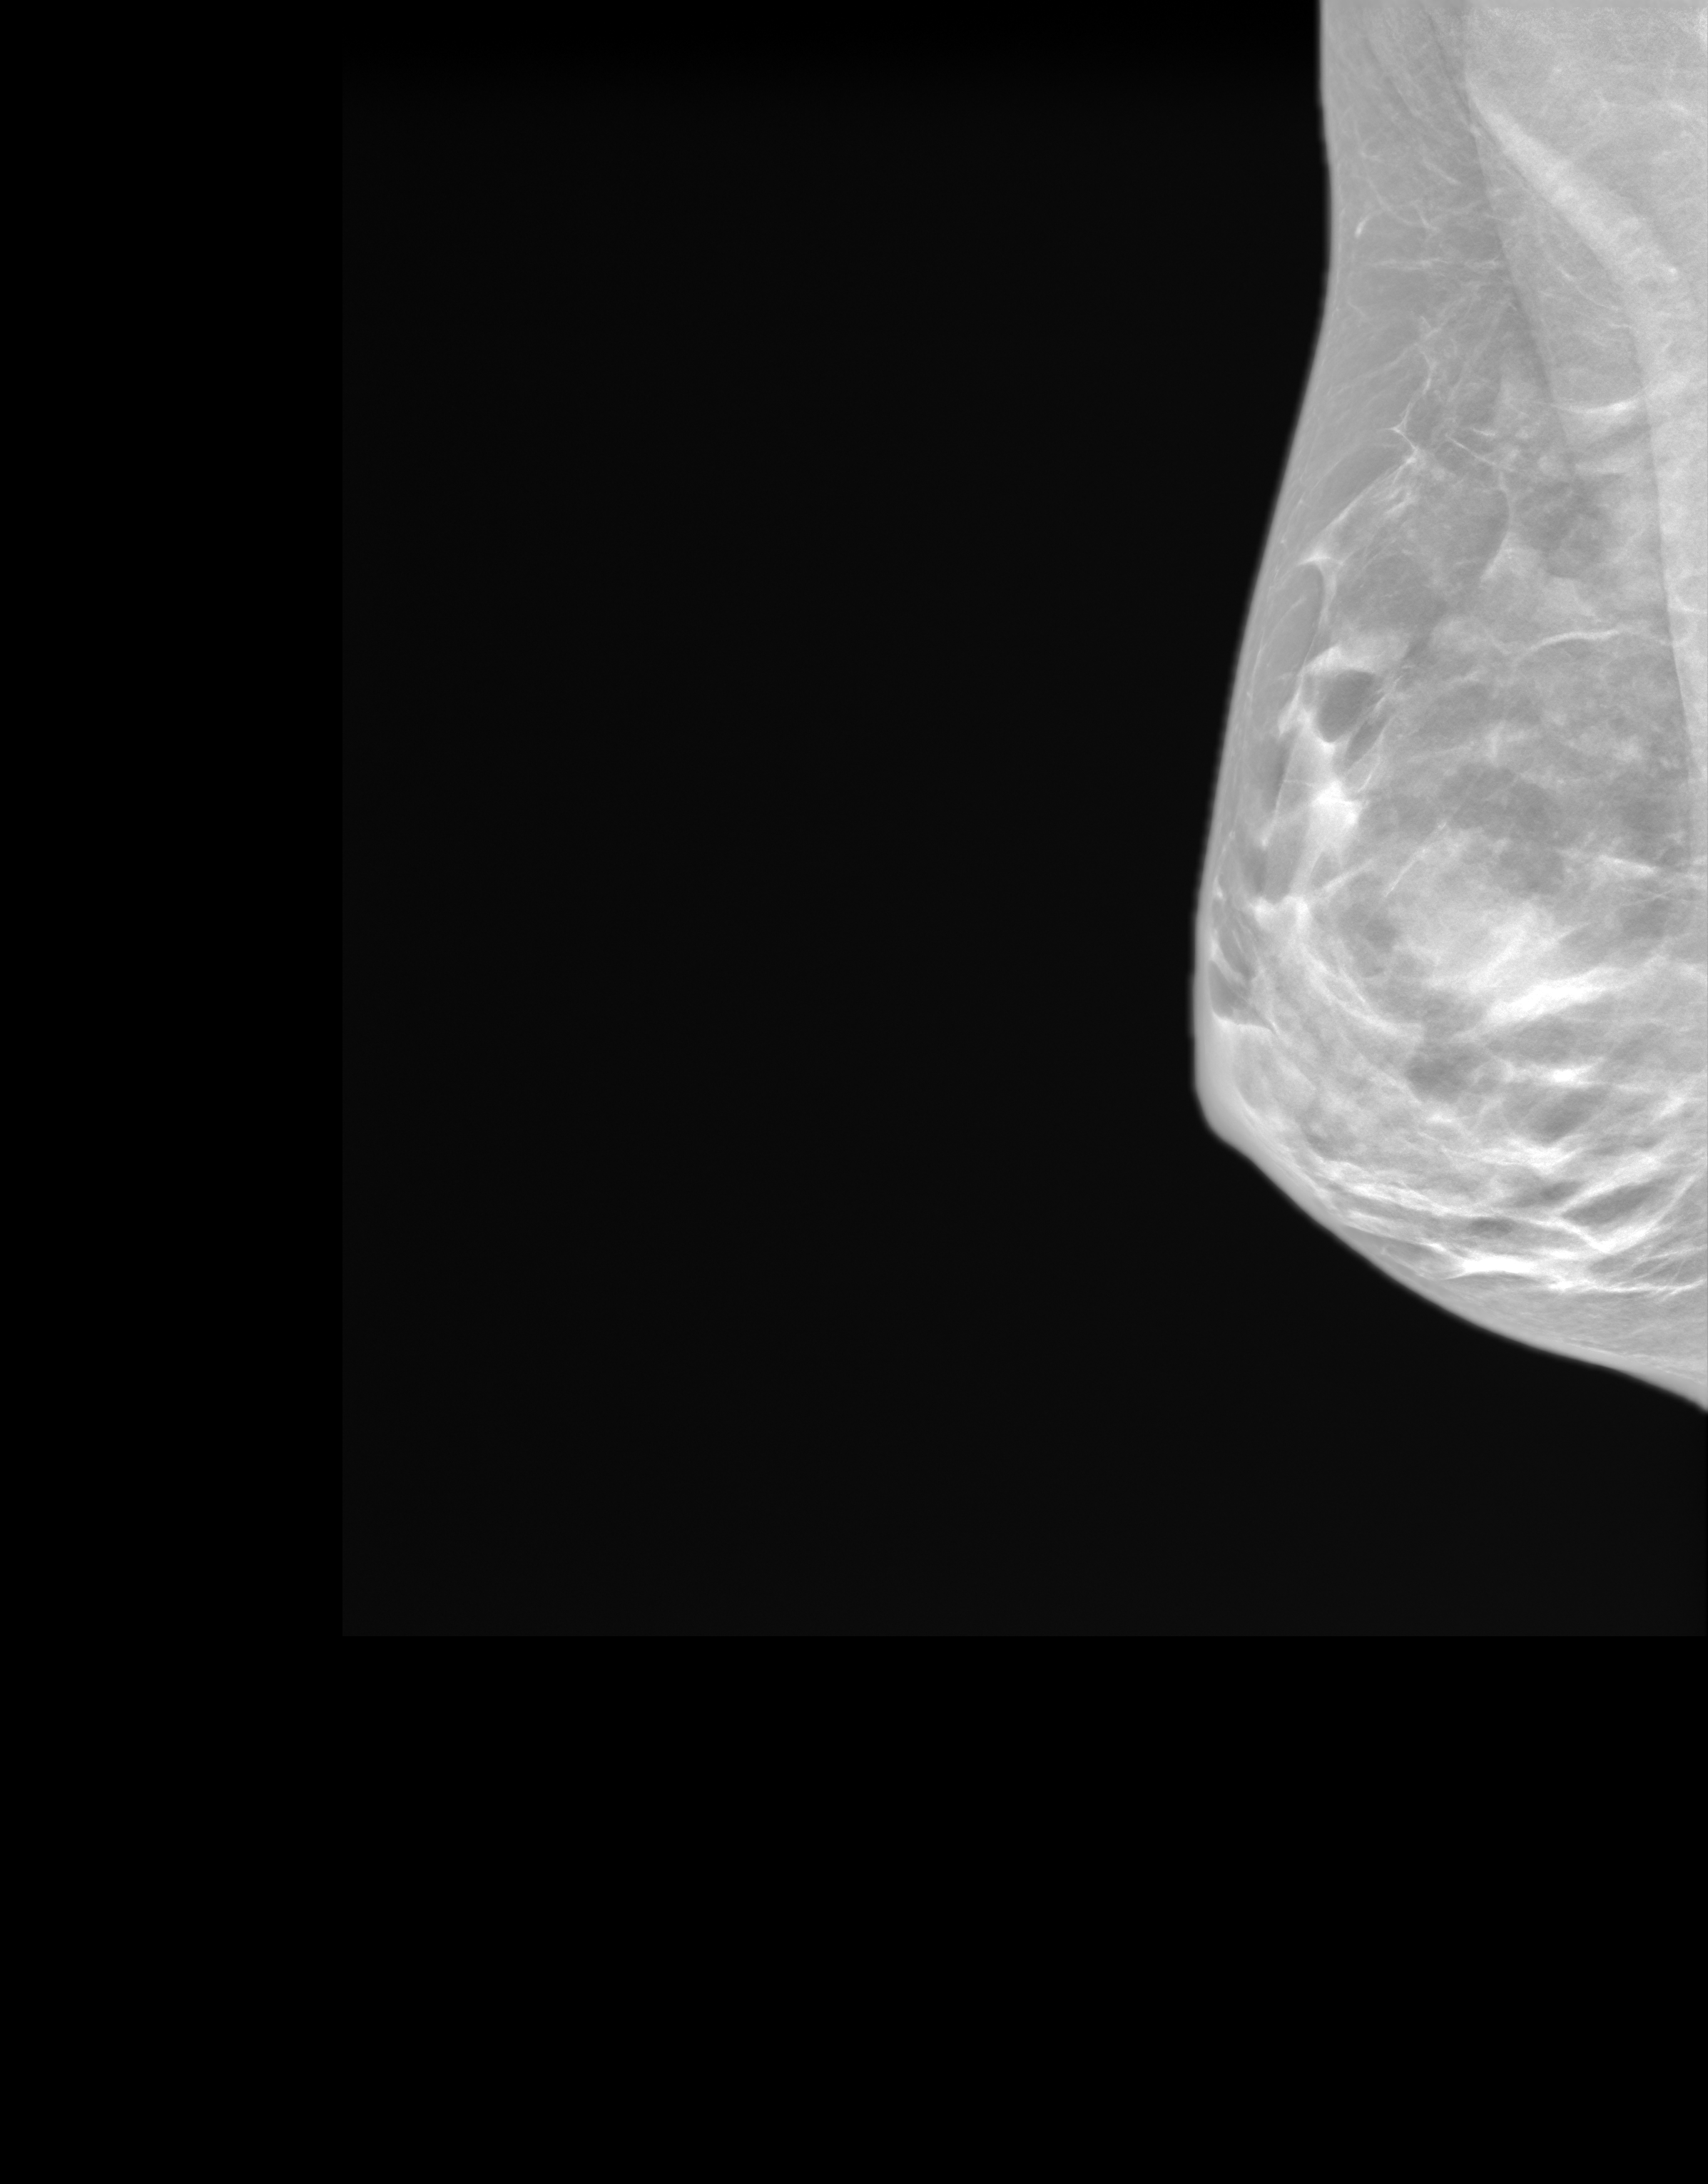
Screening examination. Patient: female, 67 years.
Image type: synthesized 2-D view from tomosynthesis. Breast: right. Projection: mediolateral oblique (MLO) view.